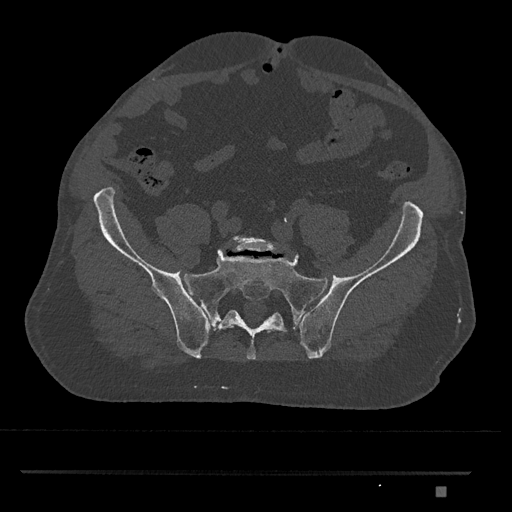
CT including the spine, one axial slice. Position 497 of 1134 along the scan axis. Bone window (W 1800 / L 400 HU). 0.5 mm slice thickness. 512 × 512 image matrix, field of view 429 × 429 mm. Male patient, age 65 years. From the clinical record (not read from this slice): primary cancer: prostate.
Outlined on this slice (semi-automatic segmentation, software-assisted and operator-edited):
- L5 vertebra: bounding box [x1, y1, x2, y2] px = [229, 236, 284, 252]